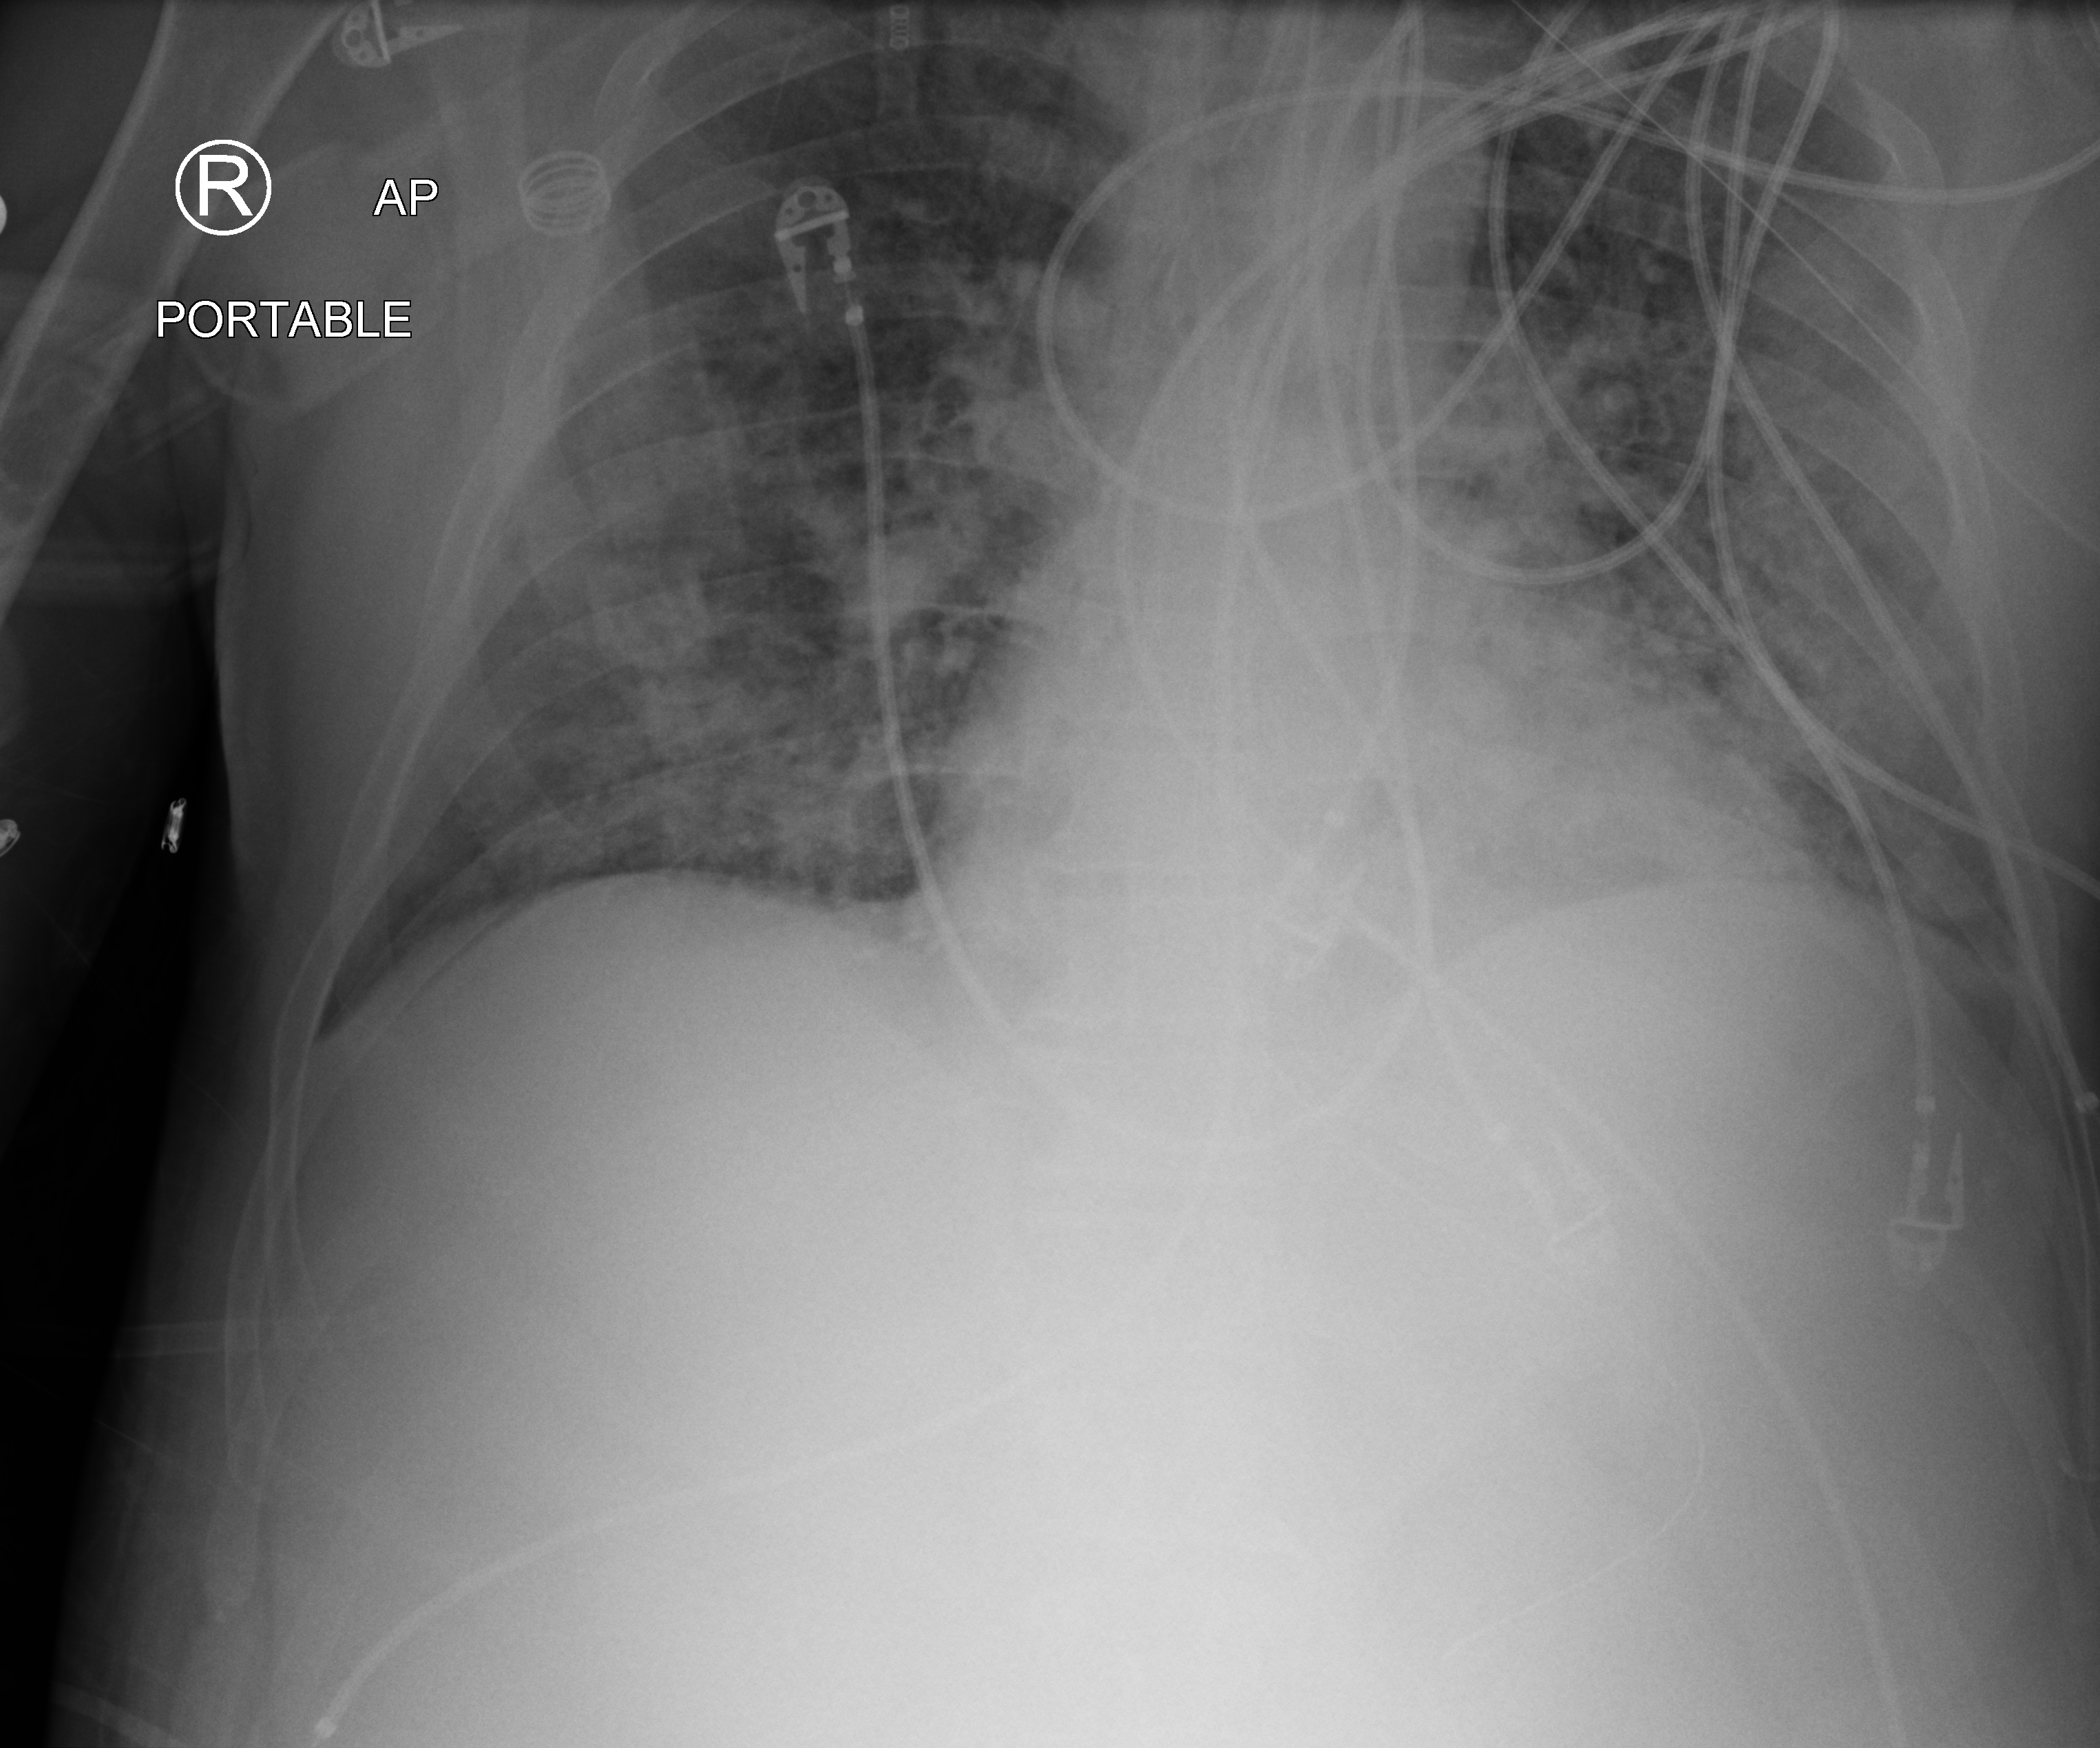
Bedside chest radiograph (computed radiography); anteroposterior (AP) projection. Patient hospitalised with COVID-19; male, aged 18–59 years.
Admission-level facts for this patient (not findings on this image; timing relative to this image not recorded): admitted to intensive care during this hospital stay: no; length of hospital stay: 19 days; mechanically ventilated during this hospital stay: yes.